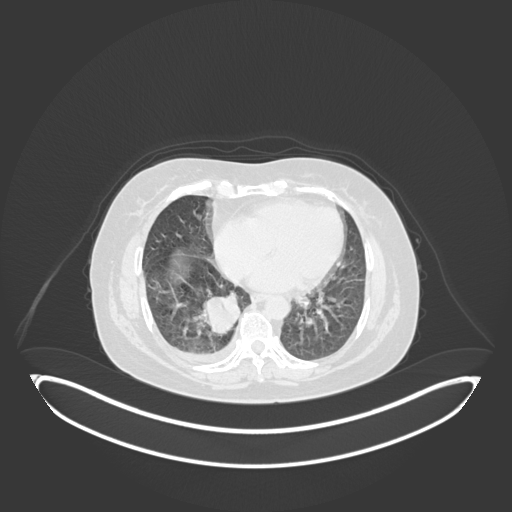
Chest CT, one axial slice. Reconstruction kernel B30f. Lung window (W 1500 / L -600 HU). 1 mm slice thickness. 512 × 512 image matrix. Patient: female, 56 years. Case-level facts recorded for this patient, not image findings: clinical TNM (as recorded): T2b N1 M0; histopathological grade: G3.
Outlined on this slice (bounding box drawn by a radiologist):
- lung tumour (recorded histology: small cell carcinoma): bounding box <198,291,254,337> (left, top, right, bottom; pixels)